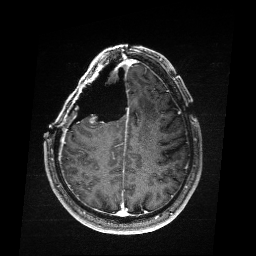
Brain MRI from a brain-tumour surgery series, one axial slice; position 67 of 176 along the scan axis; T1-weighted post-contrast; 256 × 256 image matrix. Case-level facts recorded for this patient, not image findings: histopathology: Astrocytoma; WHO grade: 4; IDH mutation: yes; tumour location: Right Frontal.
Annotated regions visible in this slice (outlined manually by an expert reader):
- residual tumour: bounding box <98,117,104,123> (left, top, right, bottom; pixels)